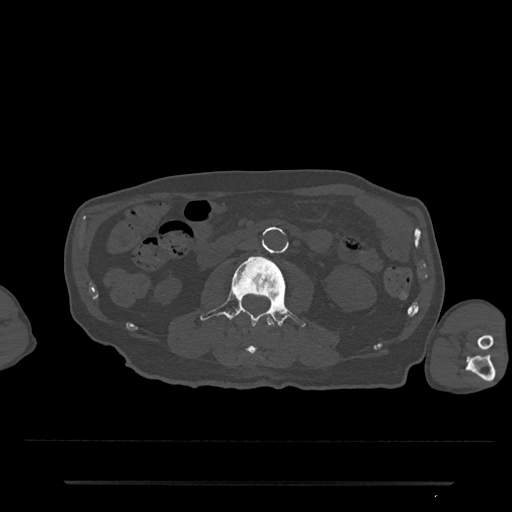
CT including the spine, one axial slice; bone window (W 1800 / L 400 HU); 512 × 512 image matrix. Patient: male, 74 years. Case-level facts recorded for this patient, not image findings: primary cancer: prostate.
Structures marked on this image (semi-automatic segmentation, software-assisted and operator-edited):
- L2 vertebra: bounding box [x1, y1, x2, y2] px = [242, 315, 277, 360]
- L3 vertebra: [200, 255, 306, 328]